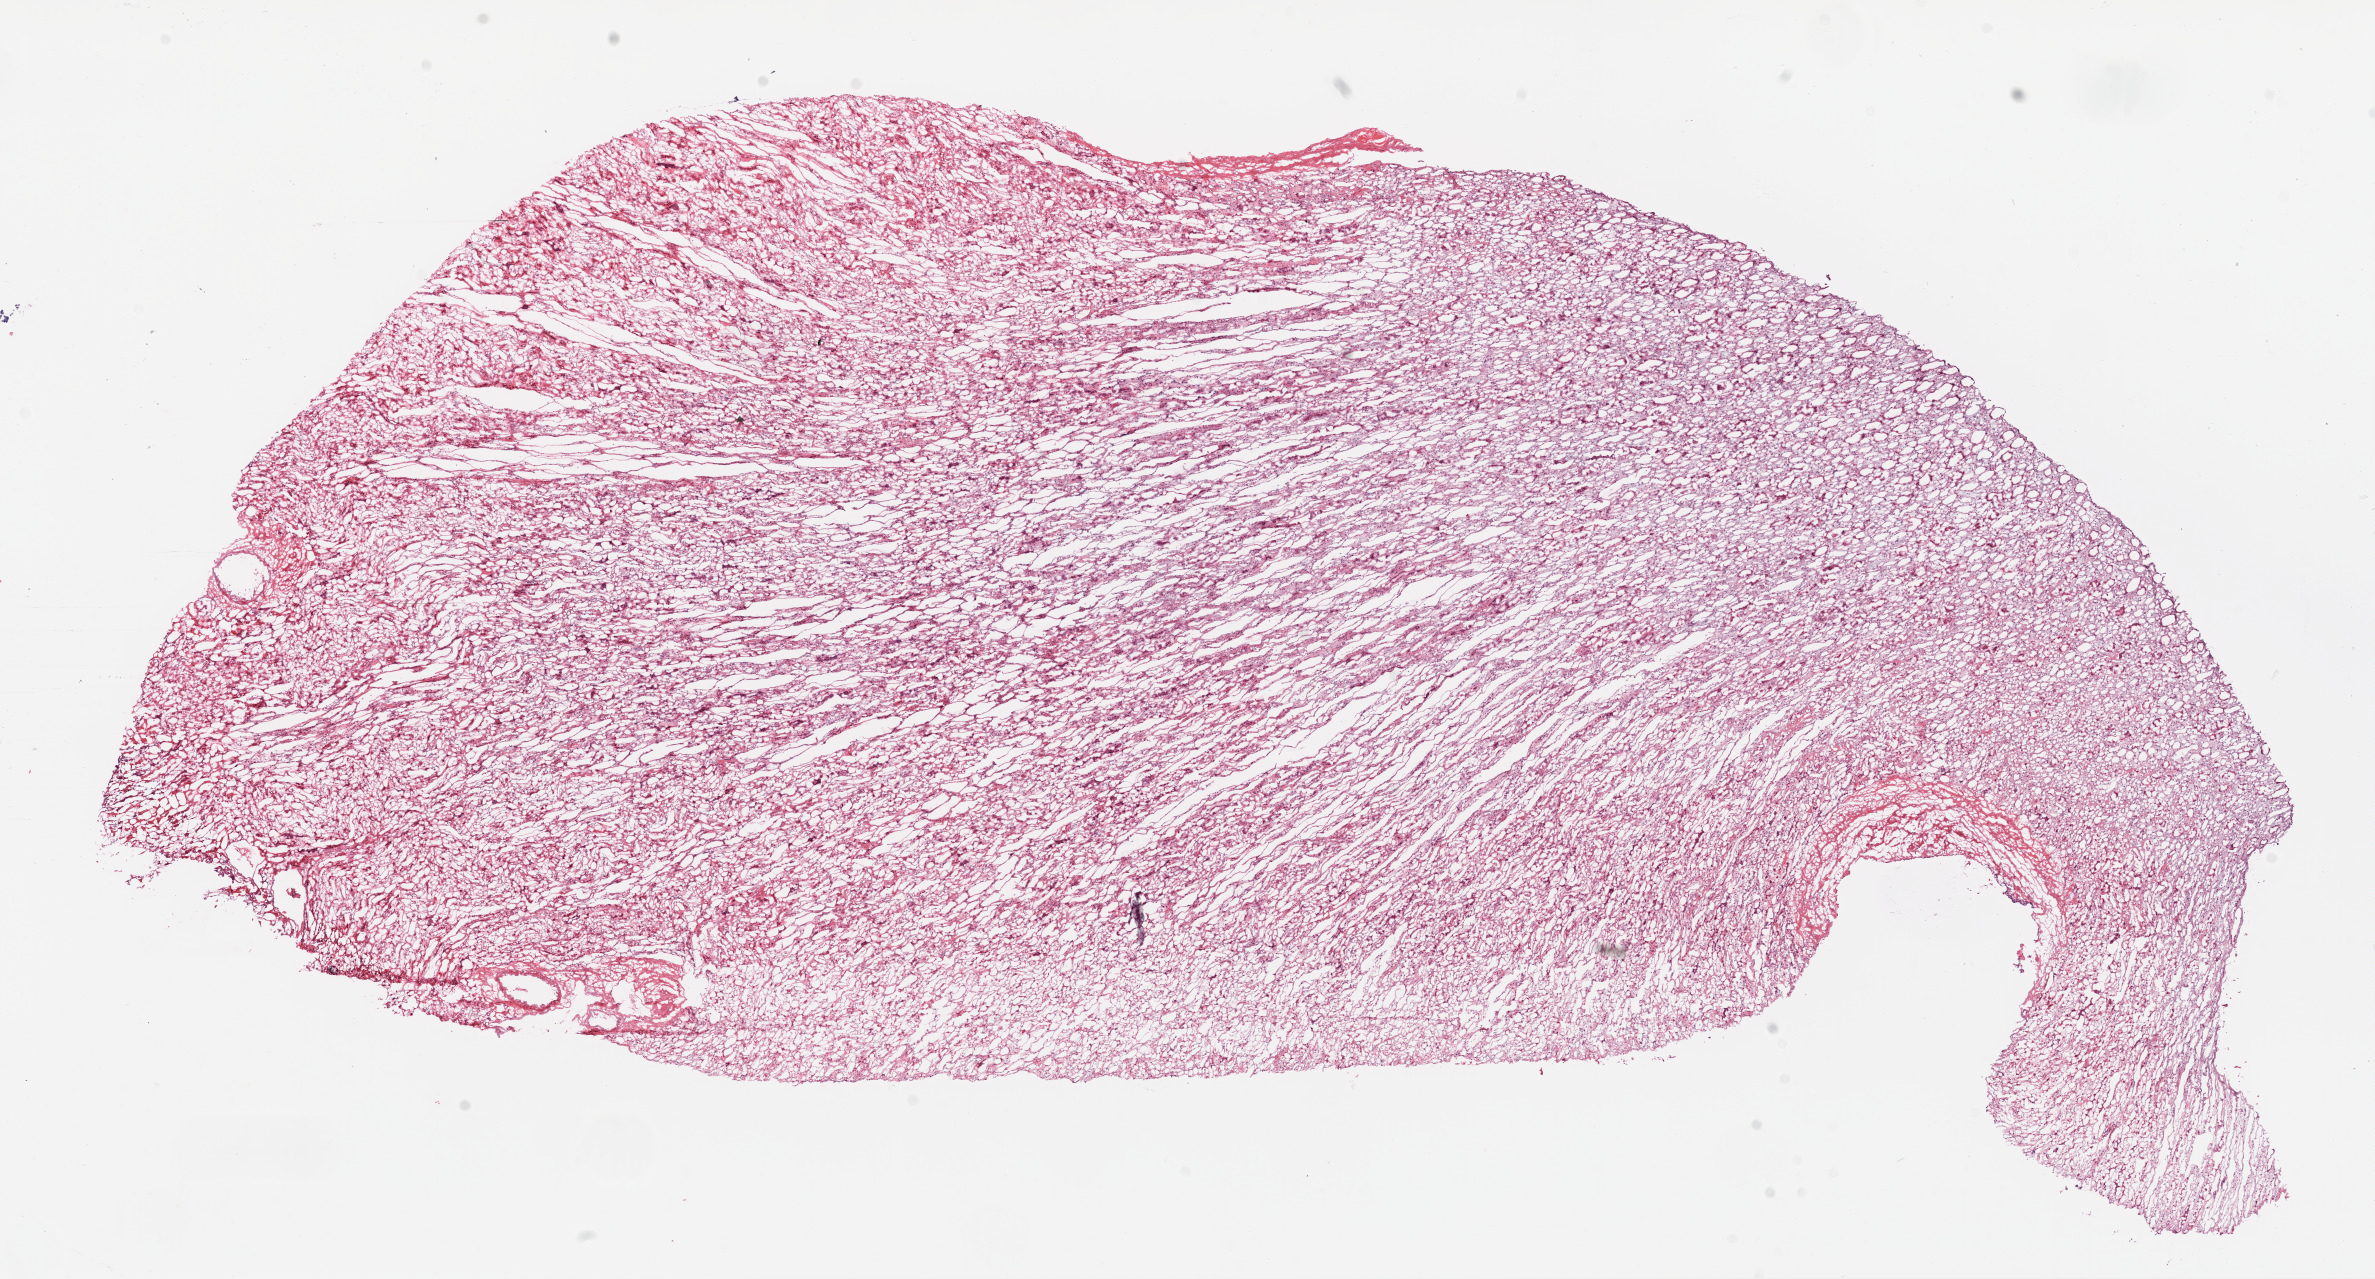
H&E-stained whole-slide image — whole scanned area (about 19.1 x 10.3 mm, slide scanned at 20x) shown as a low-resolution overview. Frozen section from the top of the tissue portion. Solid tissue normal (non-tumour tissue) sample from the kidney. Patient: male, age at initial diagnosis 43 years.
This section: solid tissue normal (non-tumour) sample from the same patient. Patient diagnosis: Clear cell adenocarcinoma, NOS.